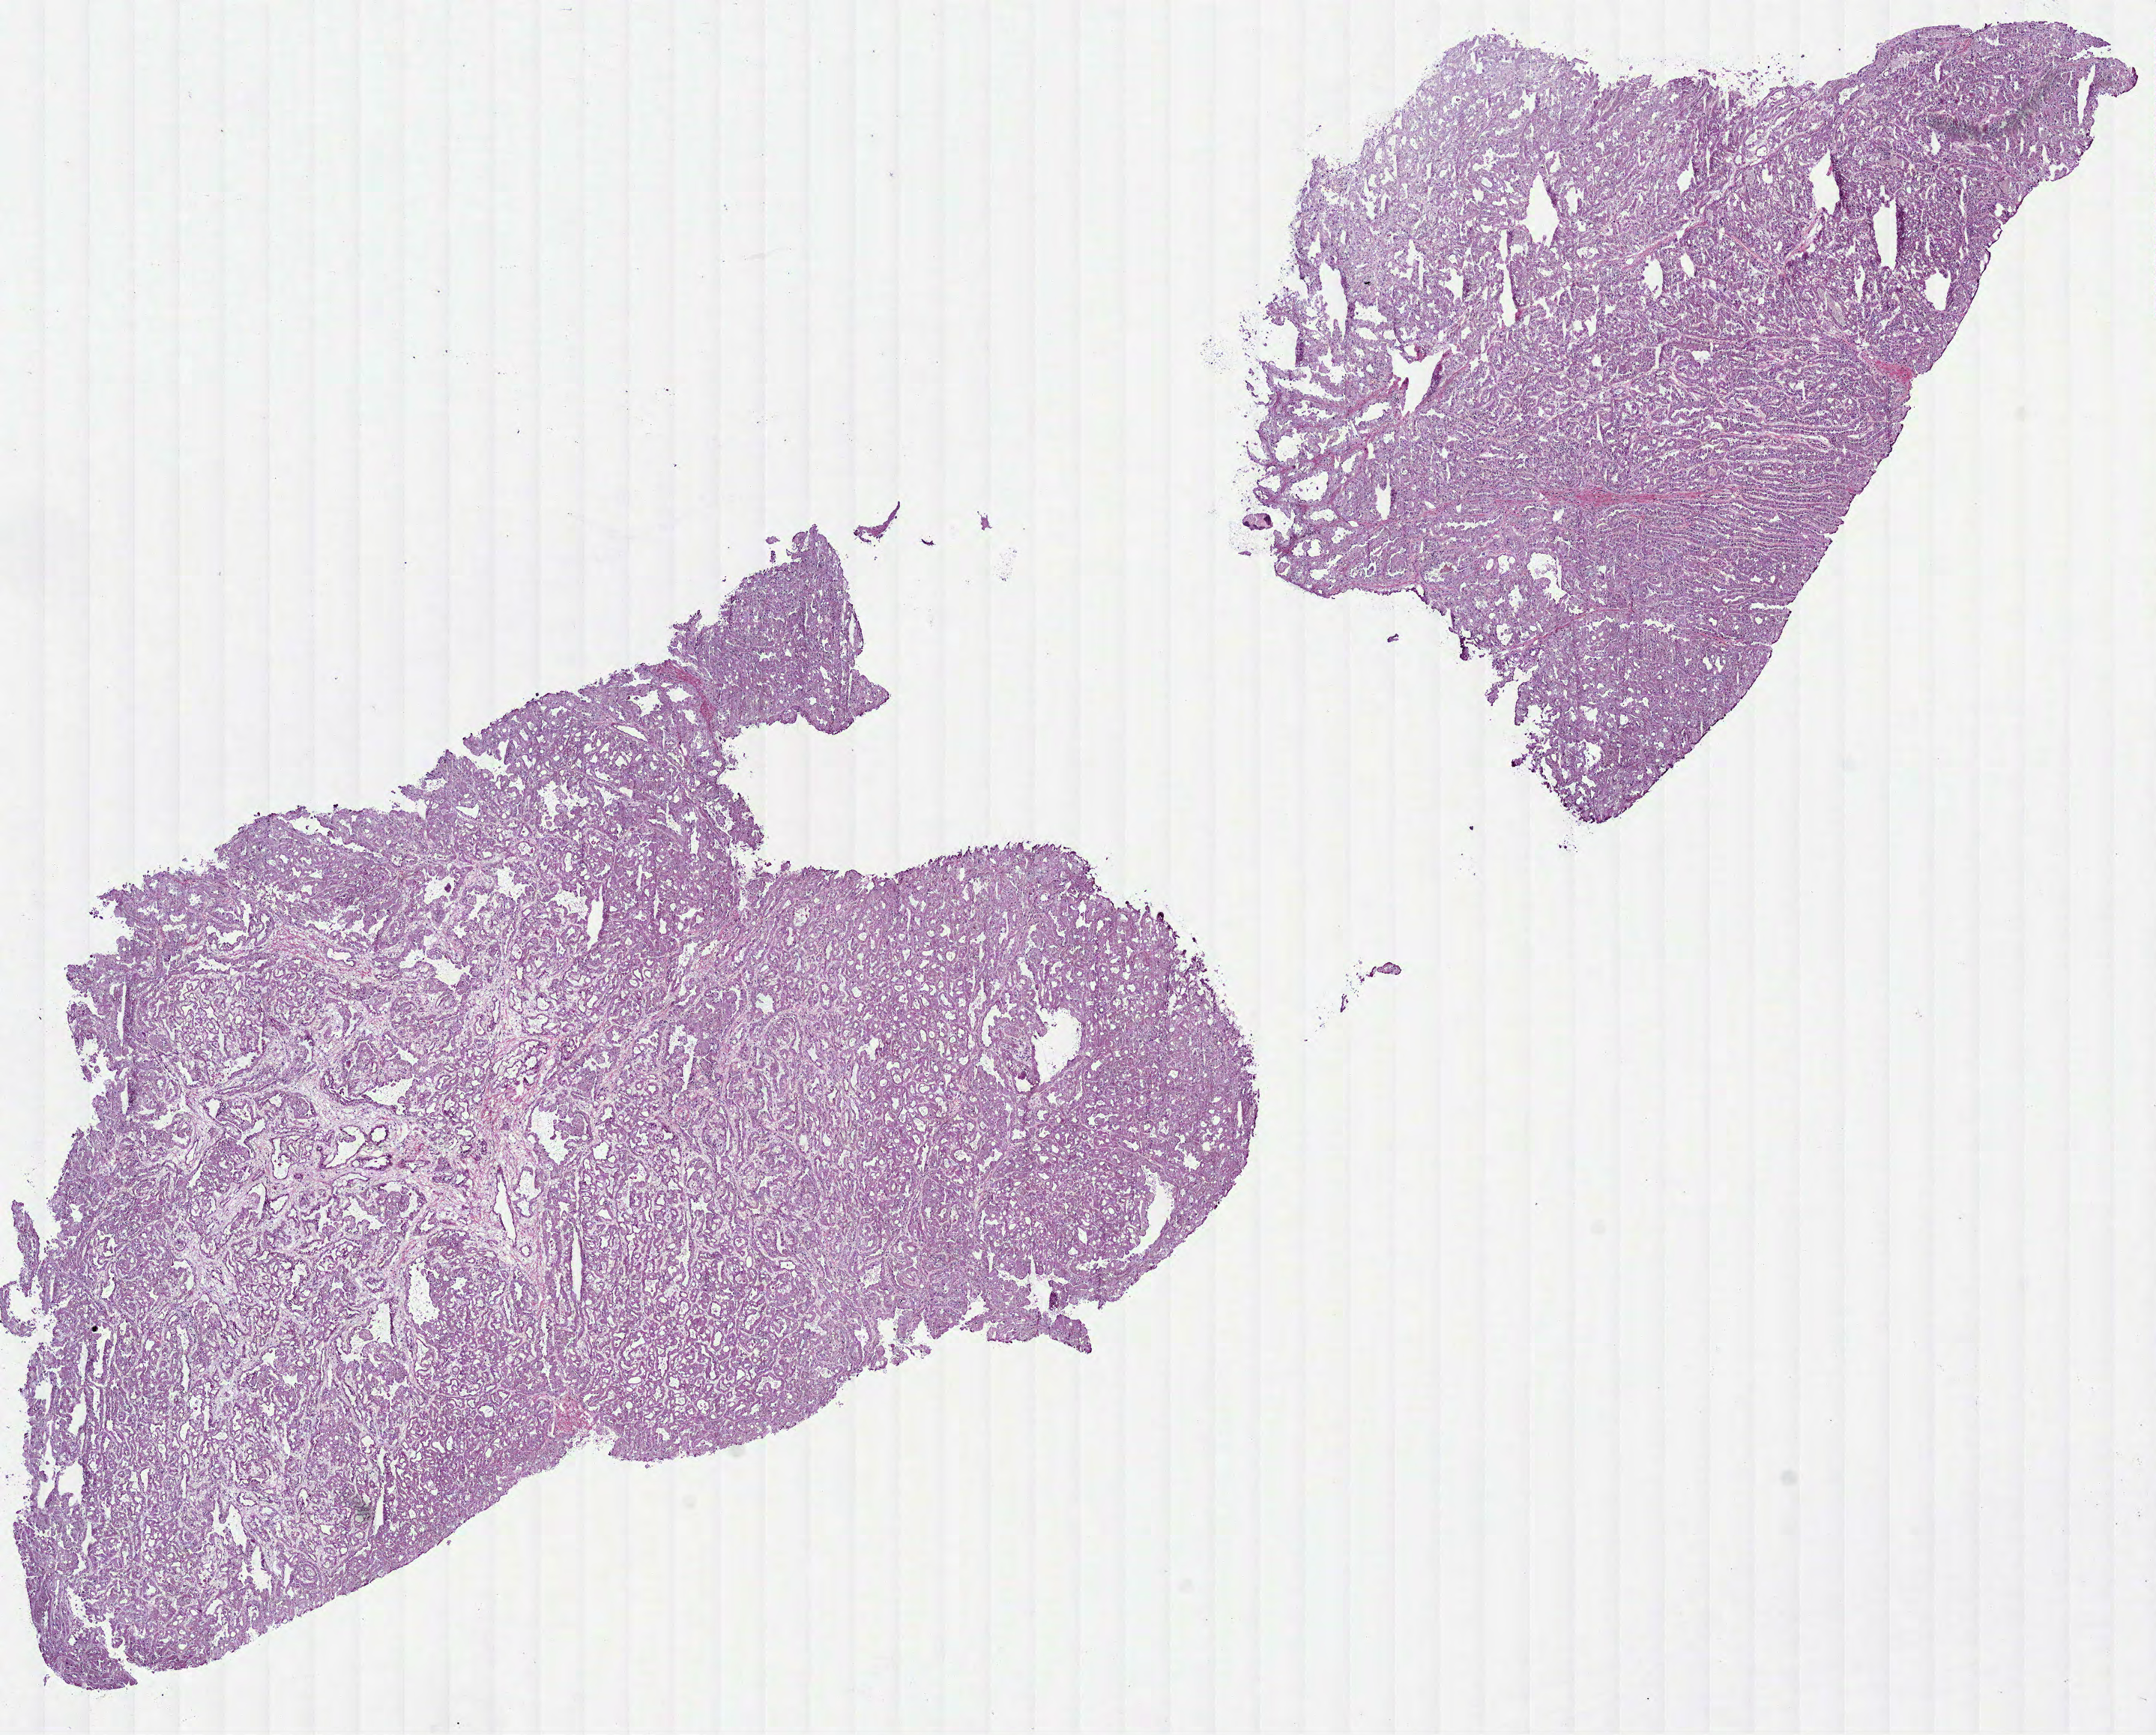
H&E whole-slide image — whole scanned area (about 11.6 x 9.3 mm, acquisition: 40x scan) shown as a low-resolution overview. Frozen section from the bottom of the tissue portion. Kidney, primary tumour sample. Patient: female, age at initial diagnosis 79 years. Composition of this section per pathologist review: tumour cells 90%, tumour nuclei 85%, normal cells 0%, stromal cells 10%, necrosis 0%.
* AJCC pathologic stage: I
* histologic diagnosis: Papillary adenocarcinoma, NOS
* laterality: right